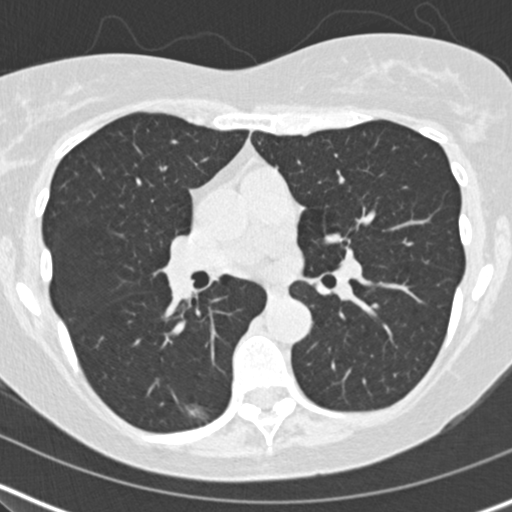
Axial slice from a low-dose chest CT screening exam; second annual screen; lung window (W 1500 / L -600 HU); 2 mm slice thickness; standard (soft-tissue) reconstruction kernel (B30f). Female participant, aged 60 years at enrolment. Former smoker at enrolment.
Expert-annotated lung lesion, bounding box [x1, y1, x2, y2] px = [169, 392, 221, 434]. The screening reader recorded 2 non-calcified nodules or masses ≥4 mm on this exam (right middle lobe, right middle lobe); which of them this box marks is not recorded.